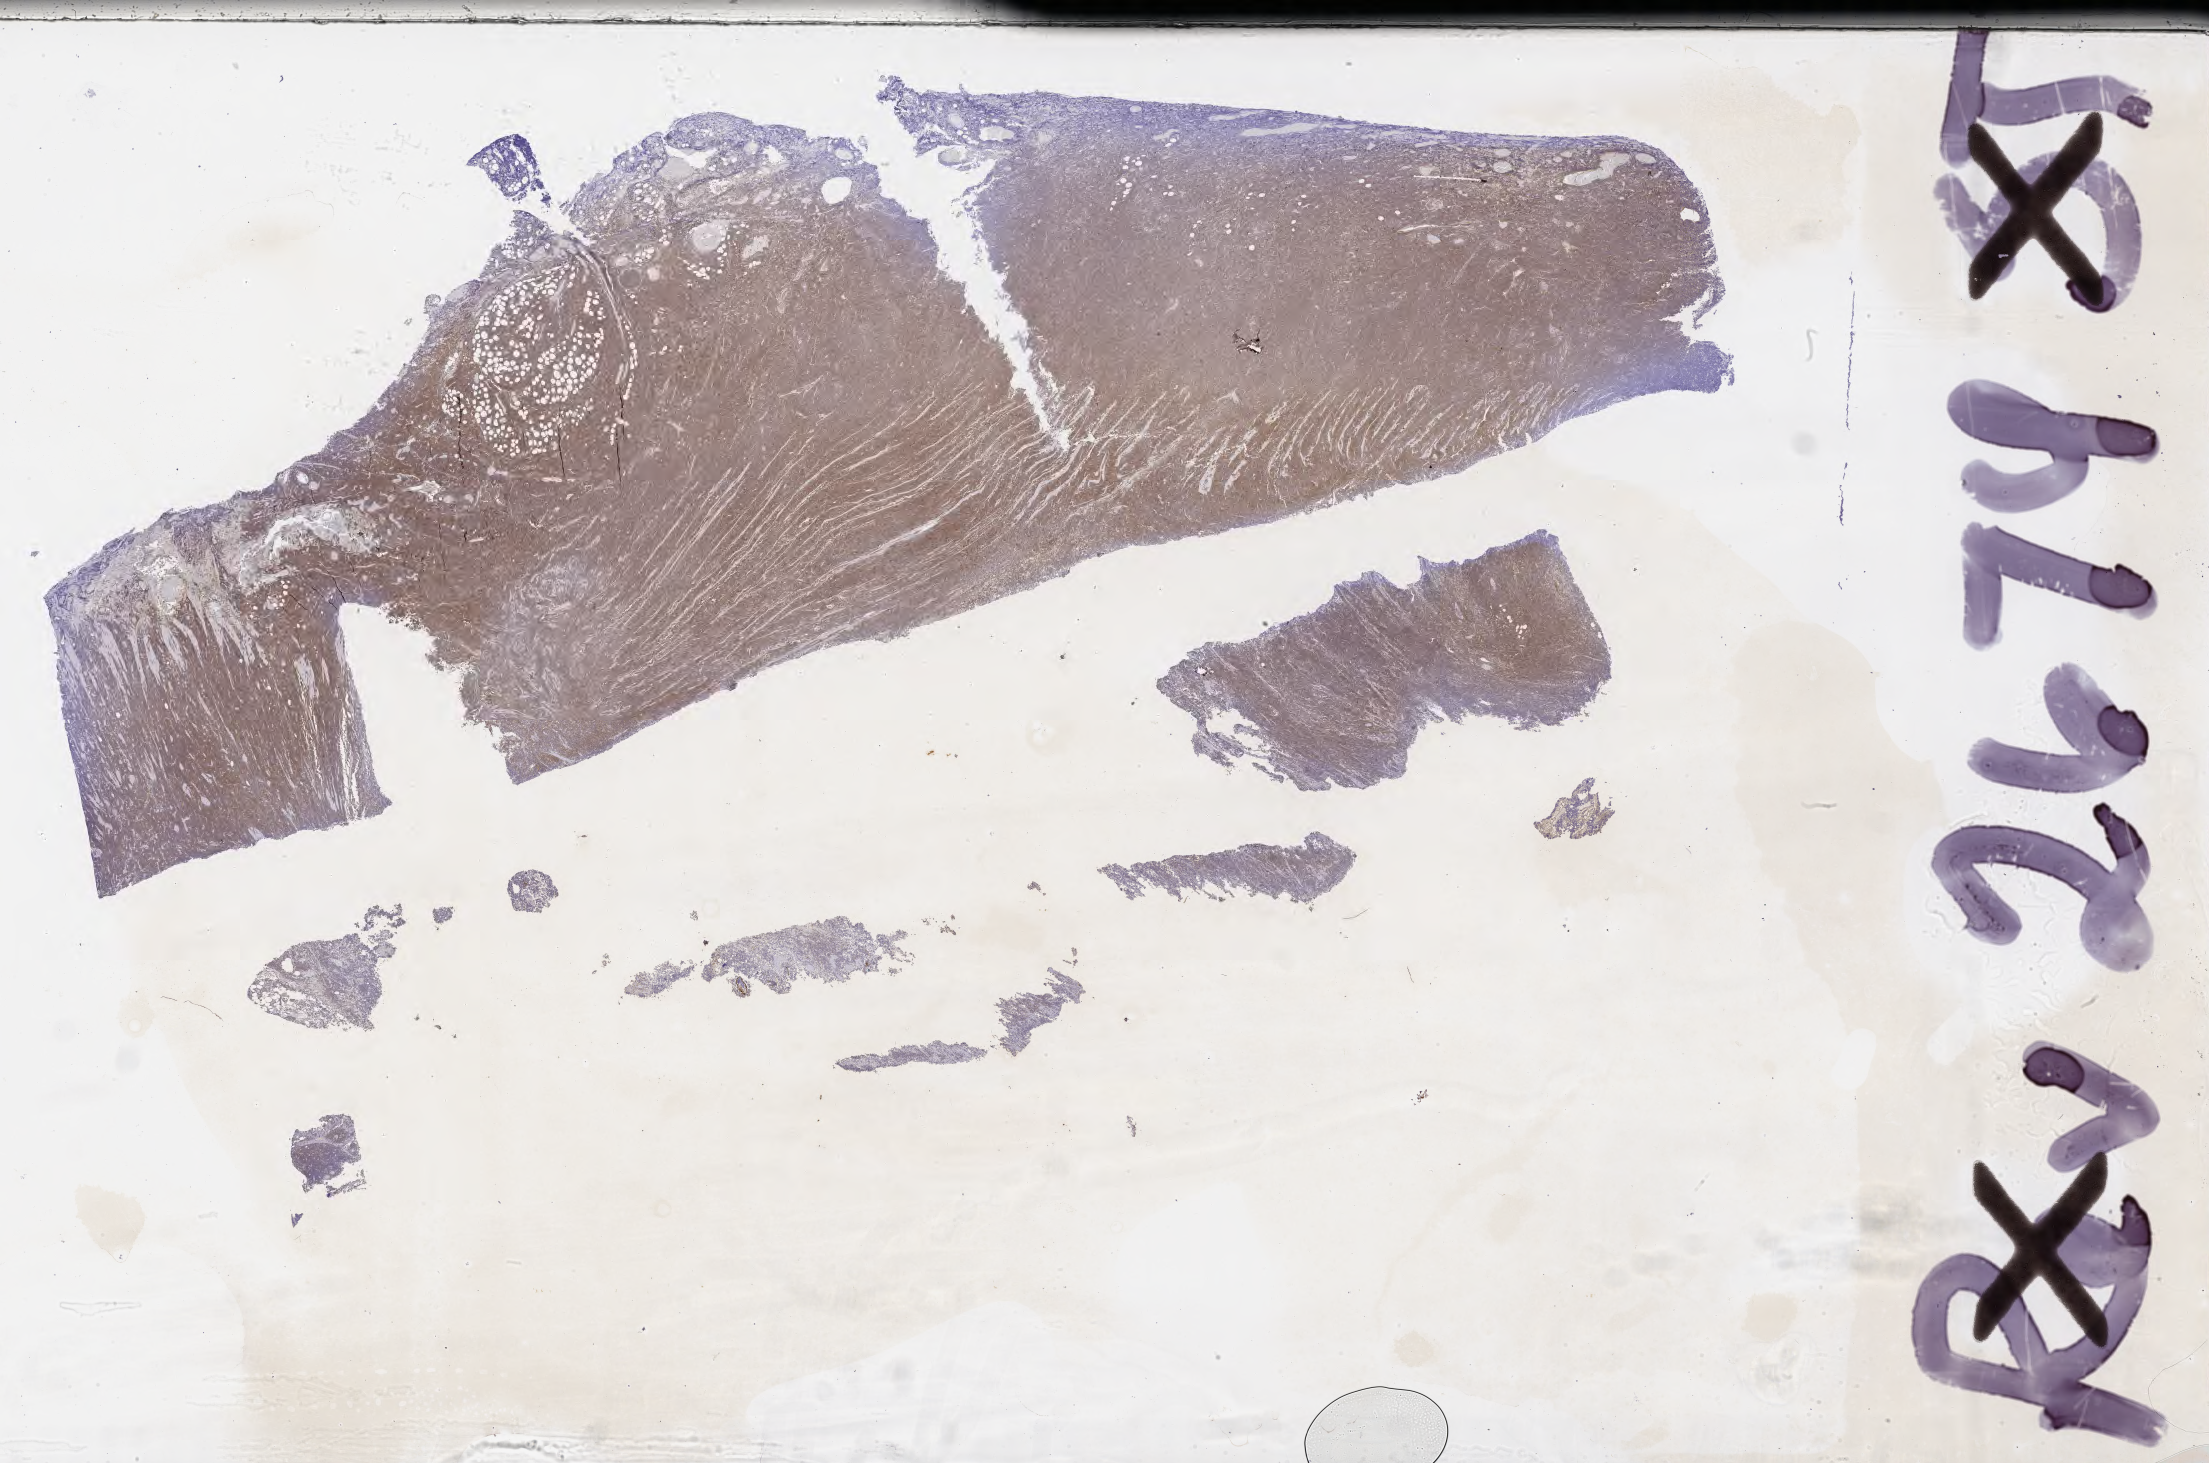
Immunohistochemistry (IHC) whole-slide image stained for CD10 — low-resolution overview of the scanned area, about 35.7 x 23.7 mm, tumor tissue. Patient male; aged 56.
• diagnosis: Burkitt lymphoma, NOS